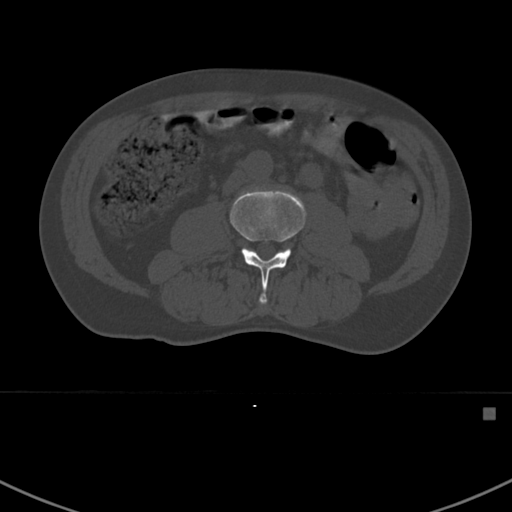
CT including the spine, one axial slice. Slice 261 of 412 in the series (ordered by position). Reconstruction kernel Br40s. Bone window (W 1800 / L 400 HU). 1.5 mm slice thickness. 512 × 512 image matrix, field of view 358 × 358 mm. Patient: male, 59 years. From the clinical record (not read from this slice): primary cancer: prostate.
Outlined on this slice (semi-automatic segmentation, software-assisted and operator-edited):
- L3 vertebra: bounding box (x1, y1, x2, y2) in pixels: (230, 187, 306, 304)